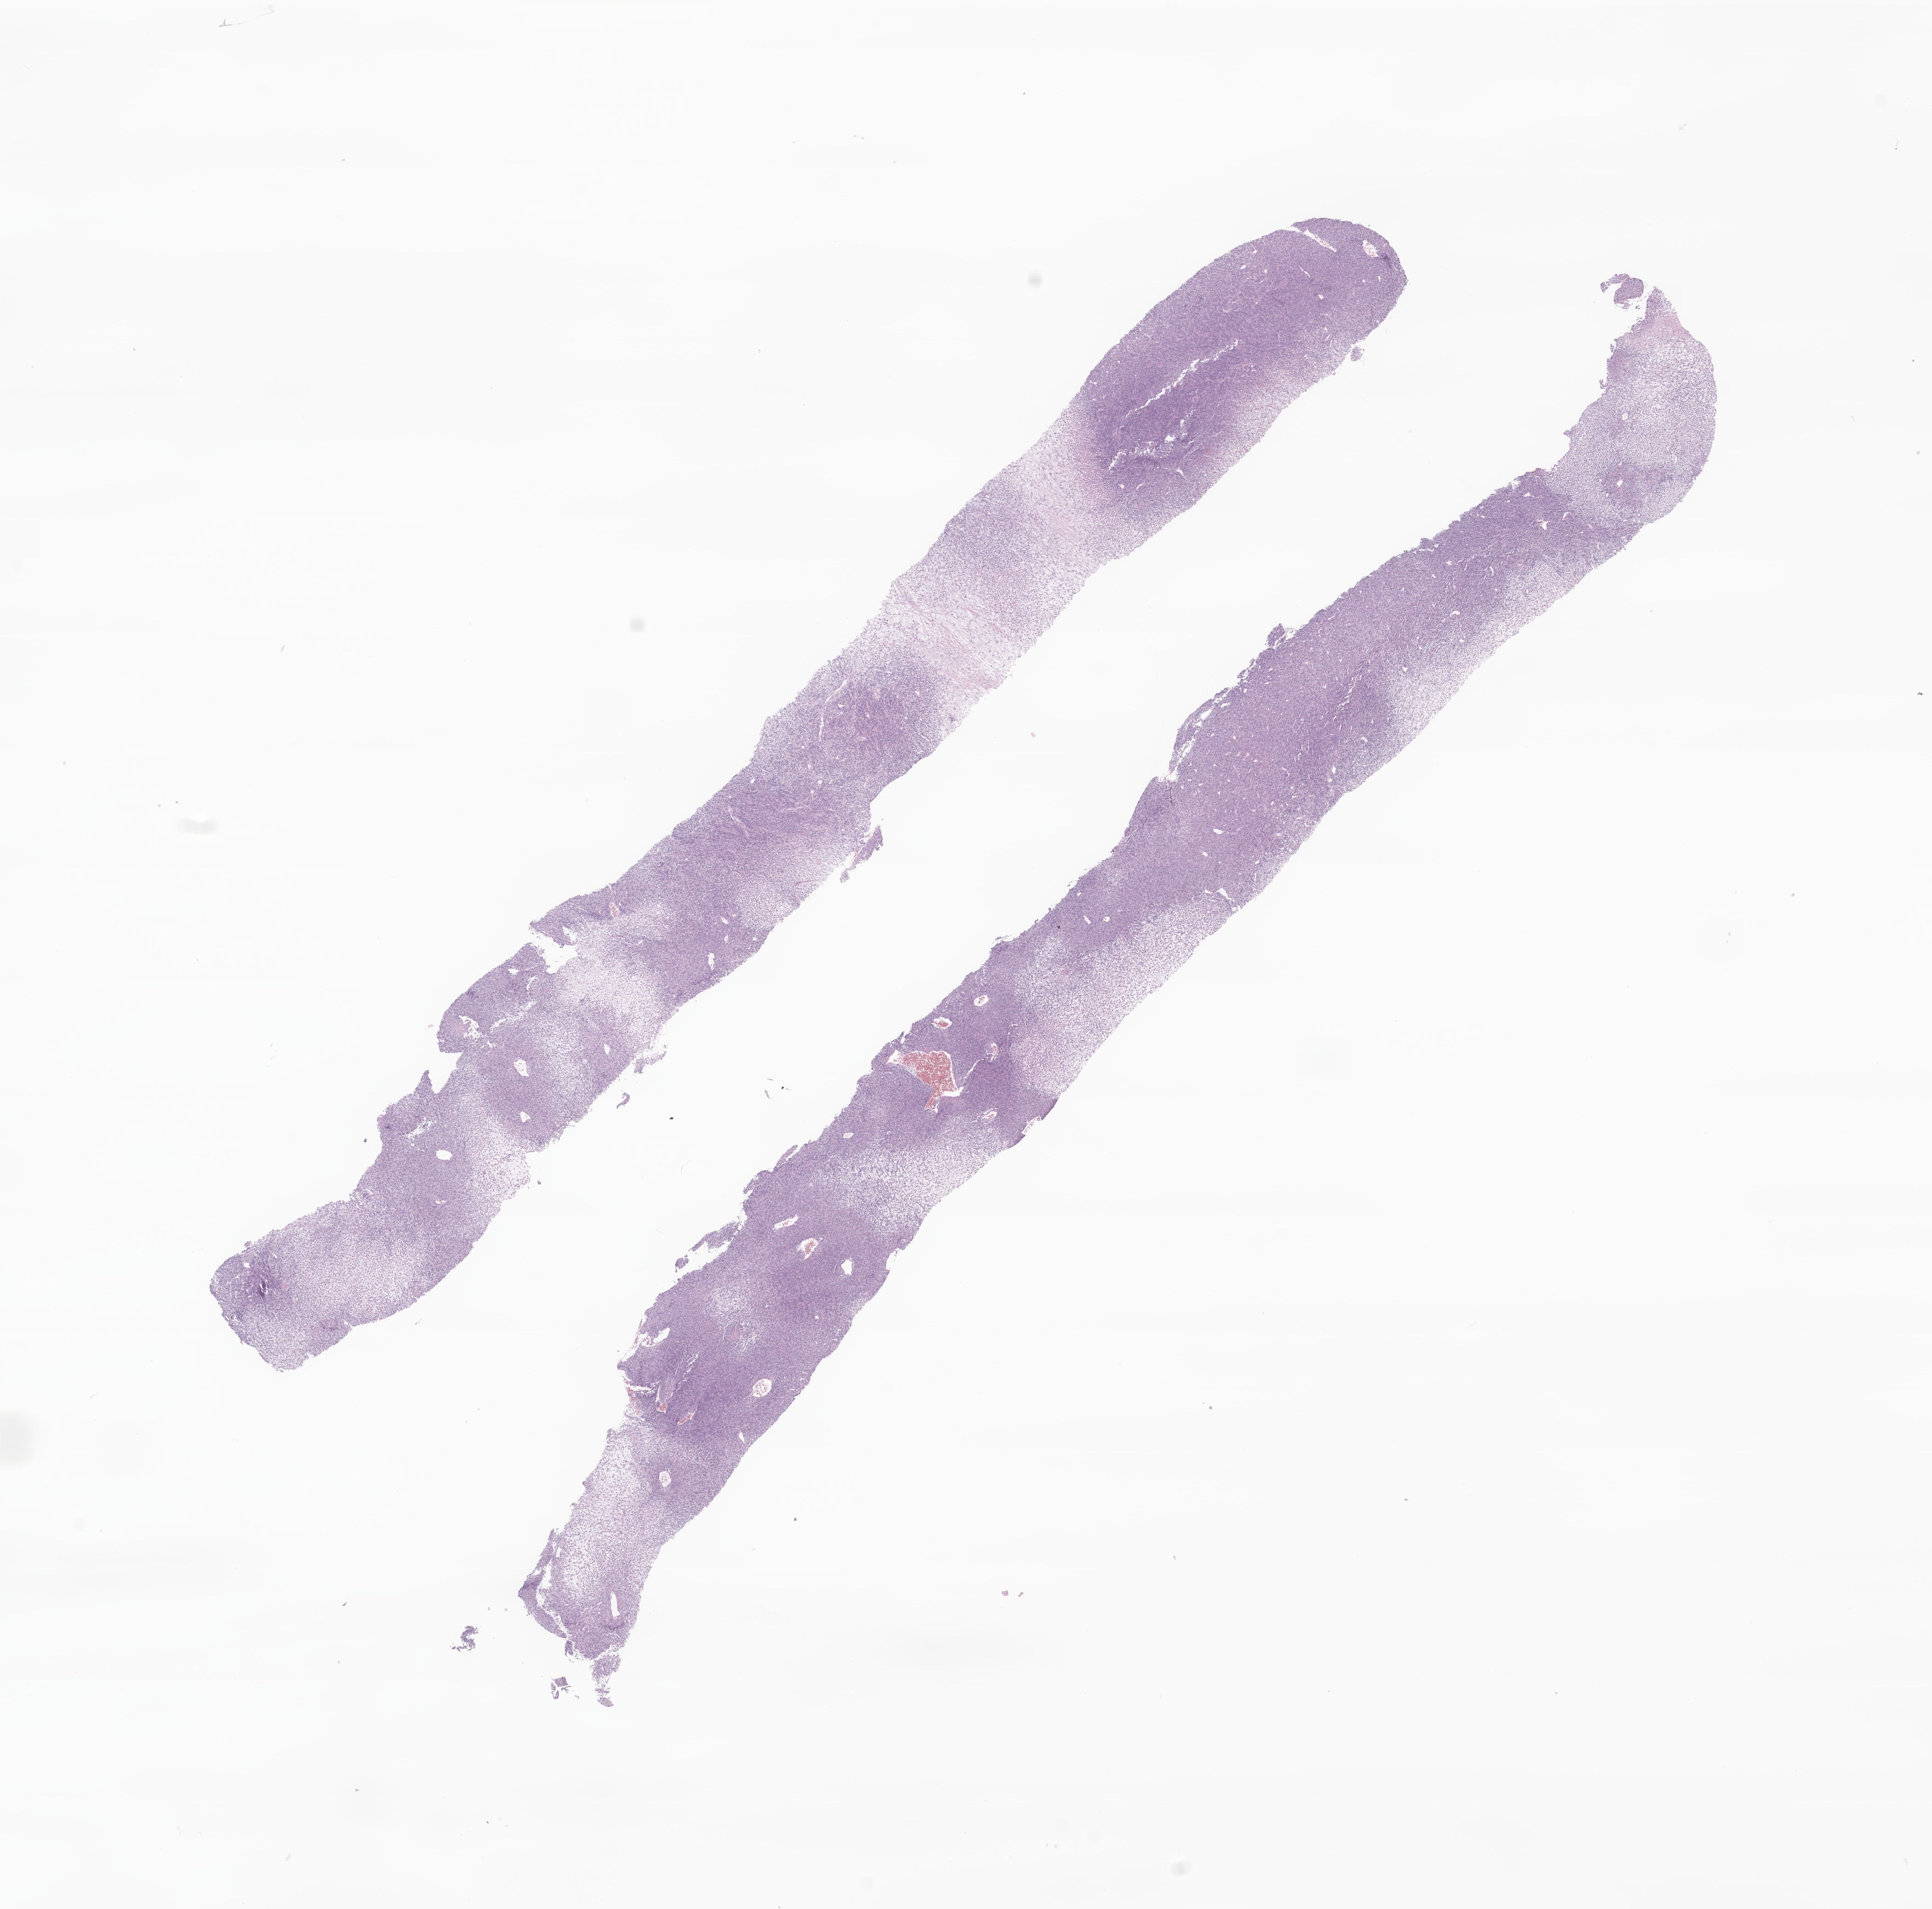
H&E whole-slide image of tumor tissue from the soft tissue, low-resolution overview of the scanned area, about 17.7 x 17.5 mm. FFPE section. Patient: male, age 135 months (11 years 3 months).
Diagnosis (ICD-O-3 morphology term): Synovial sarcoma, spindle cell.